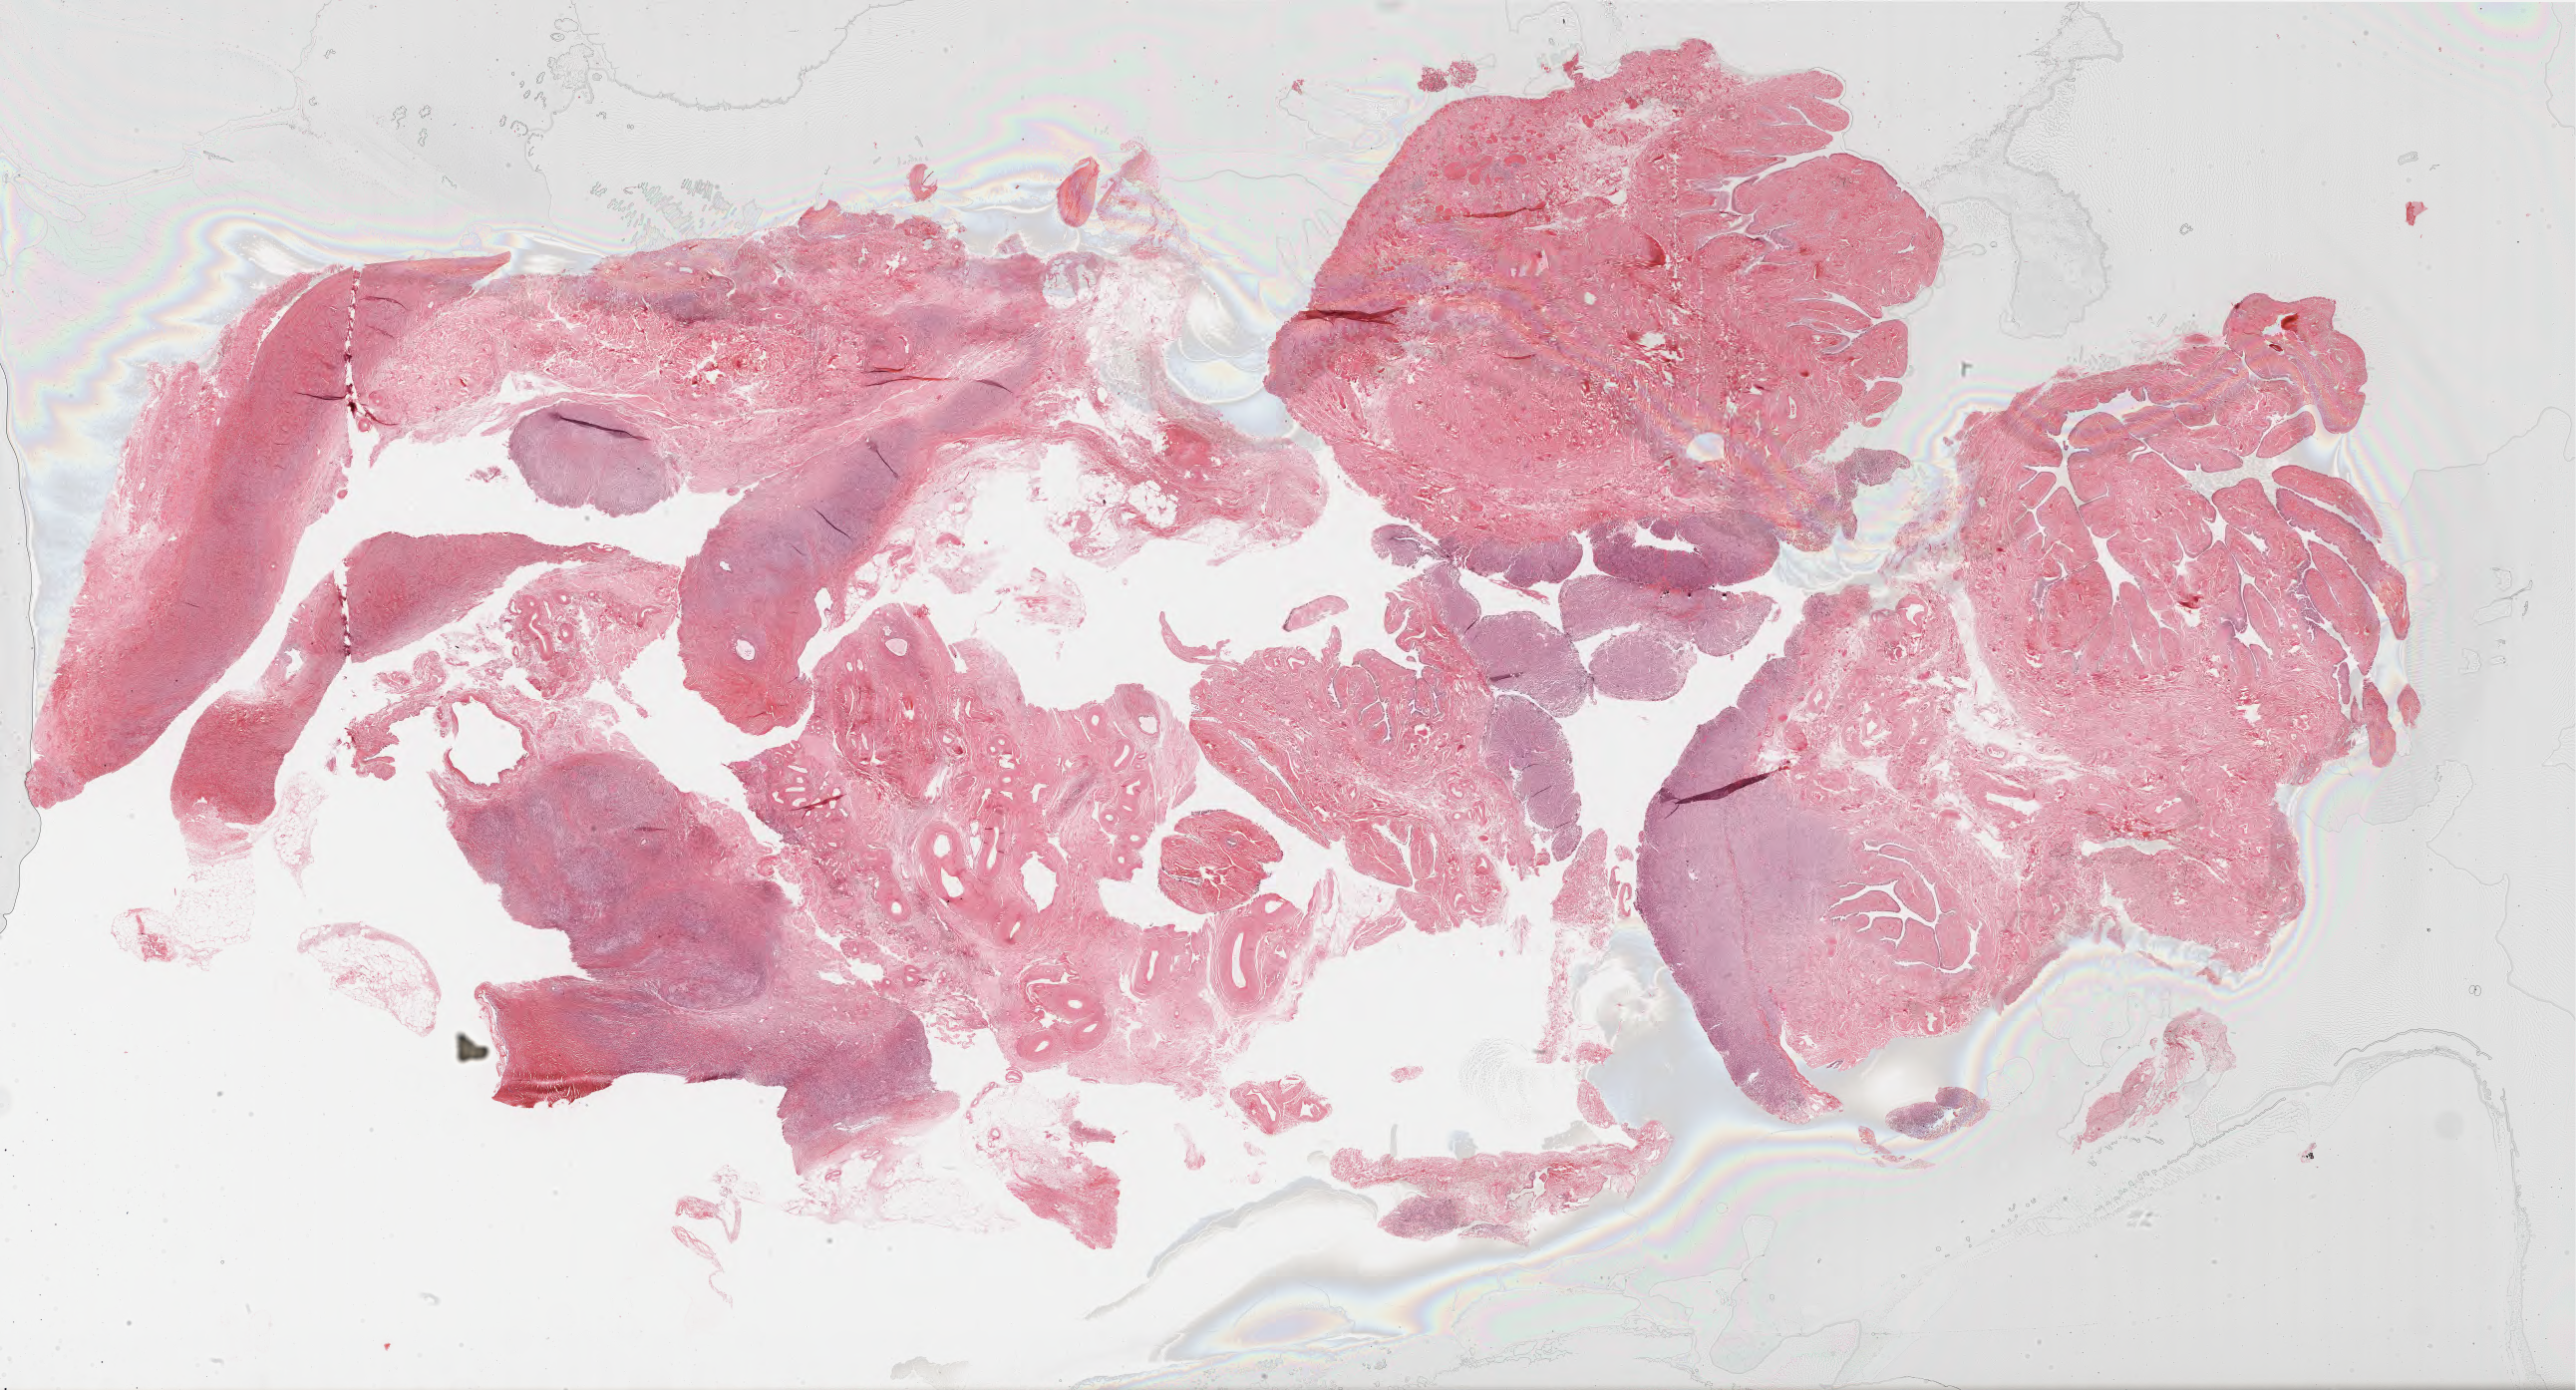
Hematoxylin and eosin (H&E) stained whole-slide image, whole scanned area (about 41.7 x 22.5 mm, from a 40x scan) shown as a low-resolution overview, formalin-fixed paraffin-embedded (FFPE) diagnostic section, primary tumour sample from the ovary. Patient: female, age at initial diagnosis 69 years. Histologic grade: G3 (poorly differentiated).
• FIGO stage: IV
• histologic diagnosis: Serous cystadenocarcinoma, NOS
• laterality: left